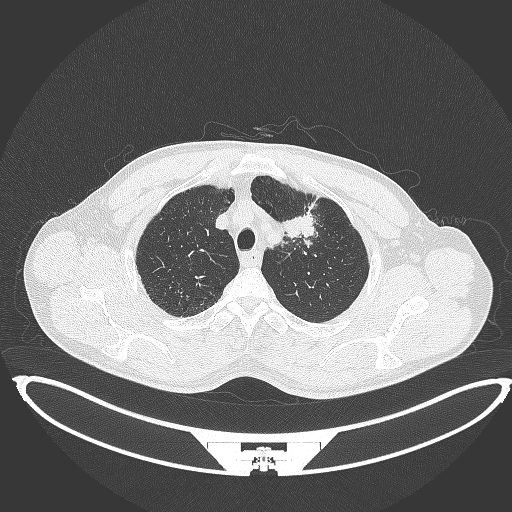
Chest CT, one axial slice; slice 365 of 395 in the series (ordered by position); 120 kVp; lung window (W 1500 / L -600 HU); 512 × 512 image matrix. Patient: male, 60 years. Case-level facts recorded for this patient, not image findings: clinical TNM (as recorded): T2a N0 M0.
Outlined on this slice (rectangle marked by the reading radiologist):
- lung tumour (recorded histology: squamous cell carcinoma): bounding box <280,212,318,240> (left, top, right, bottom; pixels)